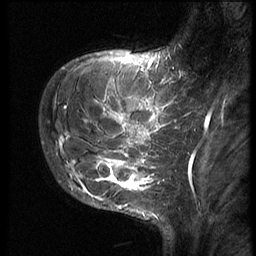
Breast MRI (dynamic contrast-enhanced), one sagittal slice; slice 13 of 62 in the series (ordered by position); 3 images stored at this slice position (order not interpretable as contrast timing); 1.5 T; TE 4.2 ms, TR 9 ms; 256 × 256 image matrix, field of view 180 × 180 mm. Female patient, age 28 years. Case-level facts recorded for this patient, not image findings: setting: breast cancer imaged before/during neoadjuvant chemotherapy.
Outlined on this slice (semi-automatic segmentation, software-assisted and operator-edited):
- analysis volume of interest (the breast-tissue region the enhancement analysis was run in; not a lesion): bounding box [x1, y1, x2, y2] px = [42, 71, 192, 197]
- tumour enhancement mask (voxels above the 140 % enhancement threshold inside the analysis volume of interest): [56, 79, 192, 192]